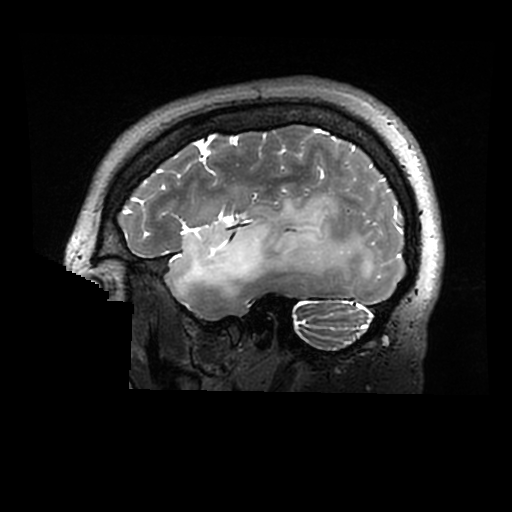
Brain MRI from a brain-tumour surgery series, one sagittal slice. Position 228 of 320 along the scan axis. 0.6 mm slice thickness. 512 × 512 image matrix. From the clinical record (not read from this slice): histopathology: Astrocytoma; WHO grade: 2; IDH mutation: yes.
Structures marked on this image (outlined manually by an expert reader):
- tumour: bounding box (x1, y1, x2, y2) in pixels: (169, 194, 379, 297)